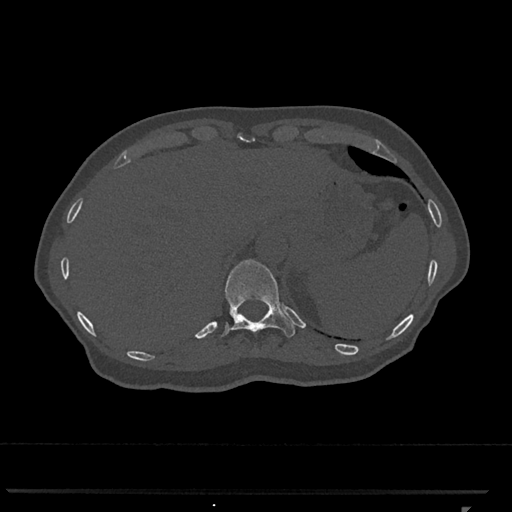
CT including the spine, one axial slice. Position 521 of 793 along the scan axis. 120 kVp. Bone window (W 1800 / L 400 HU). 512 × 512 image matrix, field of view 380 × 380 mm. Female patient, age 62 years. From the clinical record (not read from this slice): primary cancer: renal.
Annotated regions visible in this slice (semi-automatically segmented with operator editing):
- T11 vertebra: bounding box (x1, y1, x2, y2) in pixels: (221, 259, 295, 338)